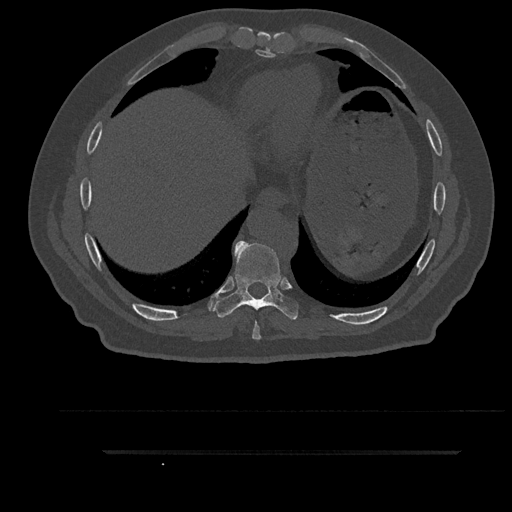
CT including the spine, one axial slice. Slice 434 of 797 in the series (ordered by position). Reconstruction kernel Br40s/3. 120 kVp. Bone window (W 1800 / L 400 HU). 0.5 mm slice thickness. 512 × 512 image matrix. Patient: male, 63 years. From the clinical record (not read from this slice): primary cancer: renal; vertebrae with lytic lesions (as recorded): T8.
Outlined on this slice (semi-automatic segmentation, software-assisted and operator-edited):
- T8 vertebra: box from (x=252, y=322) to (x=261, y=340) px
- T9 vertebra: (x=212, y=241)–(x=299, y=320)